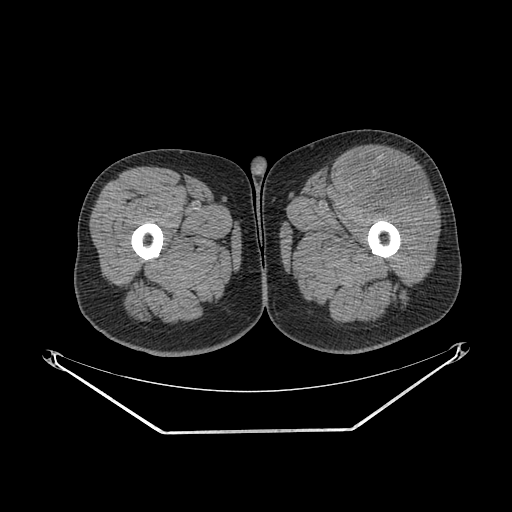
CT of an extremity soft-tissue mass (from a PET/CT study), one axial slice. Slice 243 of 267 in the series (ordered by position). Reconstruction kernel SOFT. Soft-tissue window (W 400 / L 40 HU). 512 × 512 image matrix, field of view 500 × 500 mm. Male patient. From the clinical record (not read from this slice): histological type: extraskeletal osteosarcoma; grade: high; site of the primary tumour: thigh.
Structures marked on this image (expert contour drawn on MRI and transferred to this co-registered scan by the dataset authors):
- gross tumour volume (mass): box from (x=352, y=160) to (x=428, y=213) px